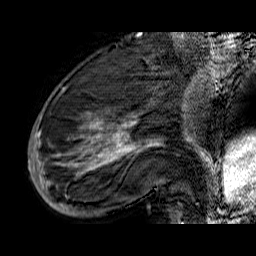
Breast MRI (dynamic contrast-enhanced), one sagittal slice. Slice 20 of 60 in the series (ordered by position). Dynamic contrast-enhanced series, time point 2 of 6 at this slice position (early post-contrast). 1.5 T. TE 6.5 ms, TR 32.9 ms. 4 mm slice thickness. 256 × 256 image matrix, field of view 200 × 200 mm. Female patient. From the clinical record (not read from this slice): setting: breast cancer imaged before/during neoadjuvant chemotherapy; receptor status: HR-positive, HER2-negative.
Structures marked on this image (semi-automatic segmentation, software-assisted and operator-edited):
- analysis volume of interest (the breast-tissue region the enhancement analysis was run in; not a lesion): bounding box (x1, y1, x2, y2) in pixels: (33, 74, 176, 210)
- tumour enhancement mask (voxels above the 100 % enhancement threshold inside the analysis volume of interest): (33, 115, 160, 210)